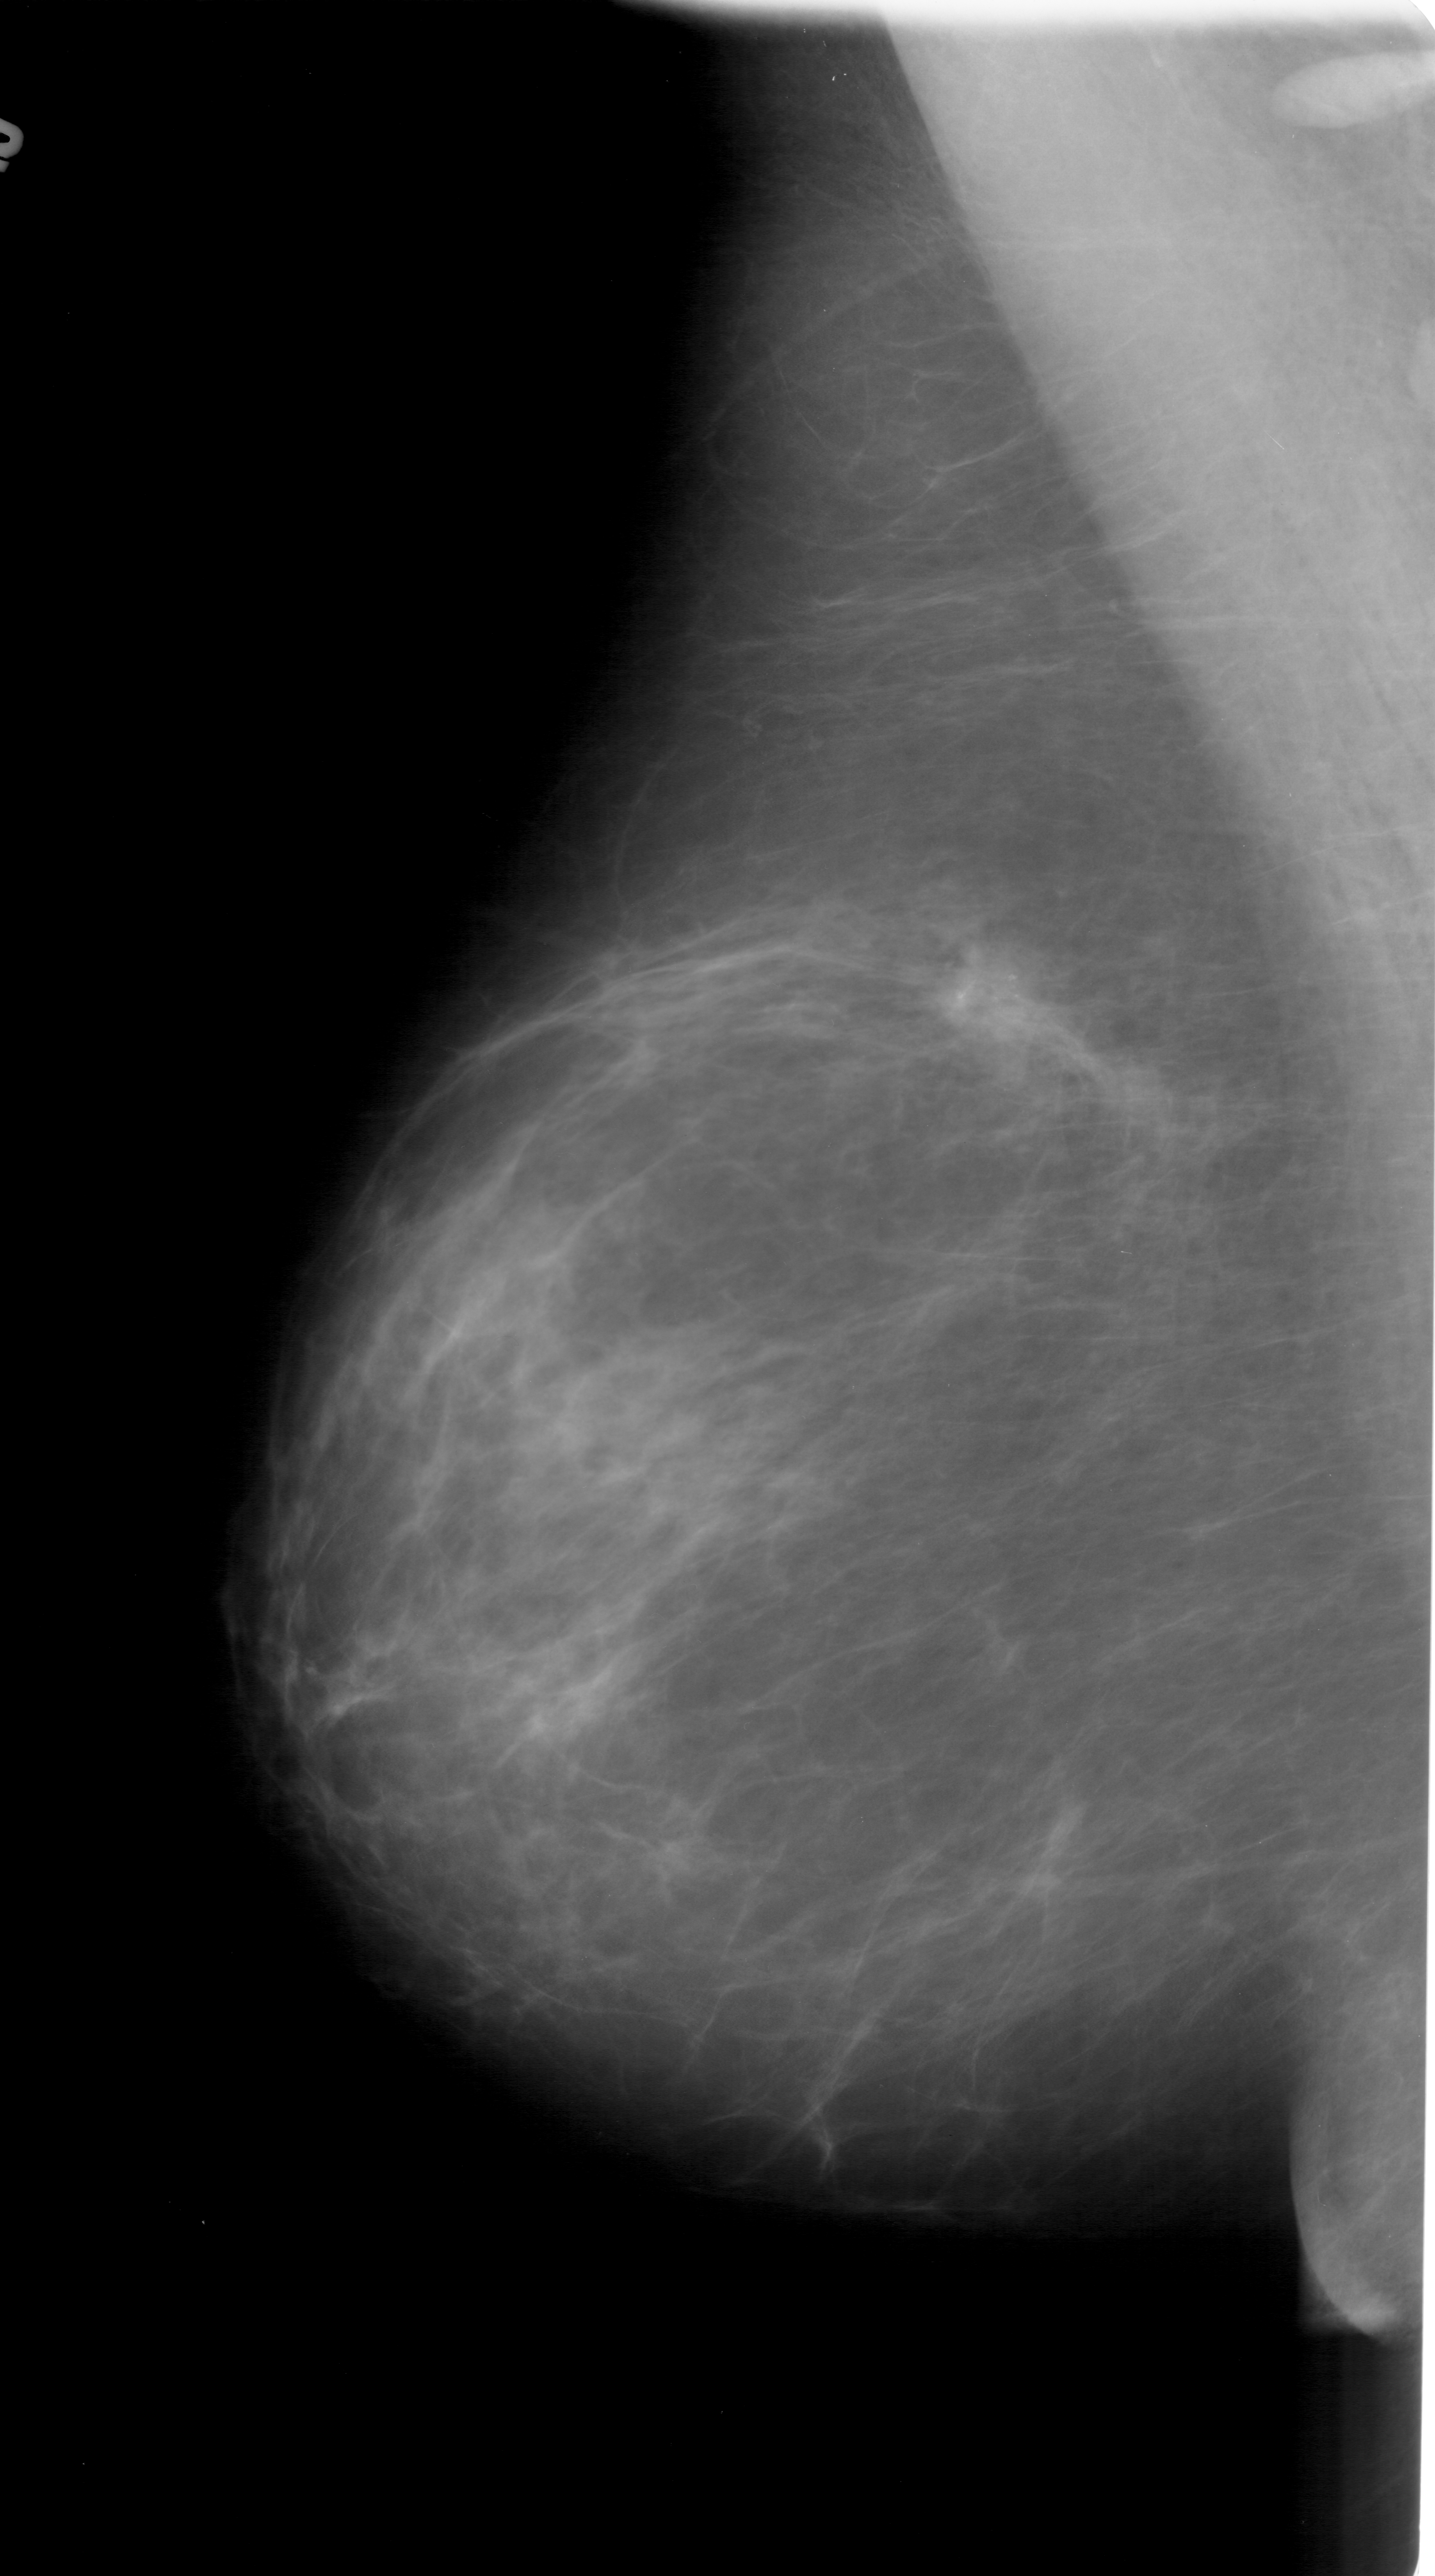
Mammogram (digitized film), left breast, MLO view.
Finding: calcifications, morphology fine linear branching, distribution linear; BI-RADS assessment category 4; subtlety rating 4 on a 1 (subtle) to 5 (obvious) scale; pathology (as recorded): malignant.